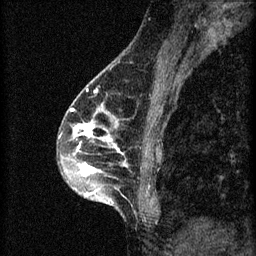
Breast MRI (dynamic contrast-enhanced), one sagittal slice; position 25 of 60 along the scan axis; 3 images stored at this slice position (order not interpretable as contrast timing); 1.5 T; TE 4.2 ms, TR 8.2 ms; 2 mm slice thickness; 256 × 256 image matrix, field of view 180 × 180 mm. Patient: female, 45 years.
Structures marked on this image (semi-automatically segmented with operator editing):
- analysis volume of interest (the breast-tissue region the enhancement analysis was run in; not a lesion): bounding box <58,104,157,215> (left, top, right, bottom; pixels)
- tumour enhancement mask (voxels above the 70 % enhancement threshold inside the analysis volume of interest): <70,104,125,199>